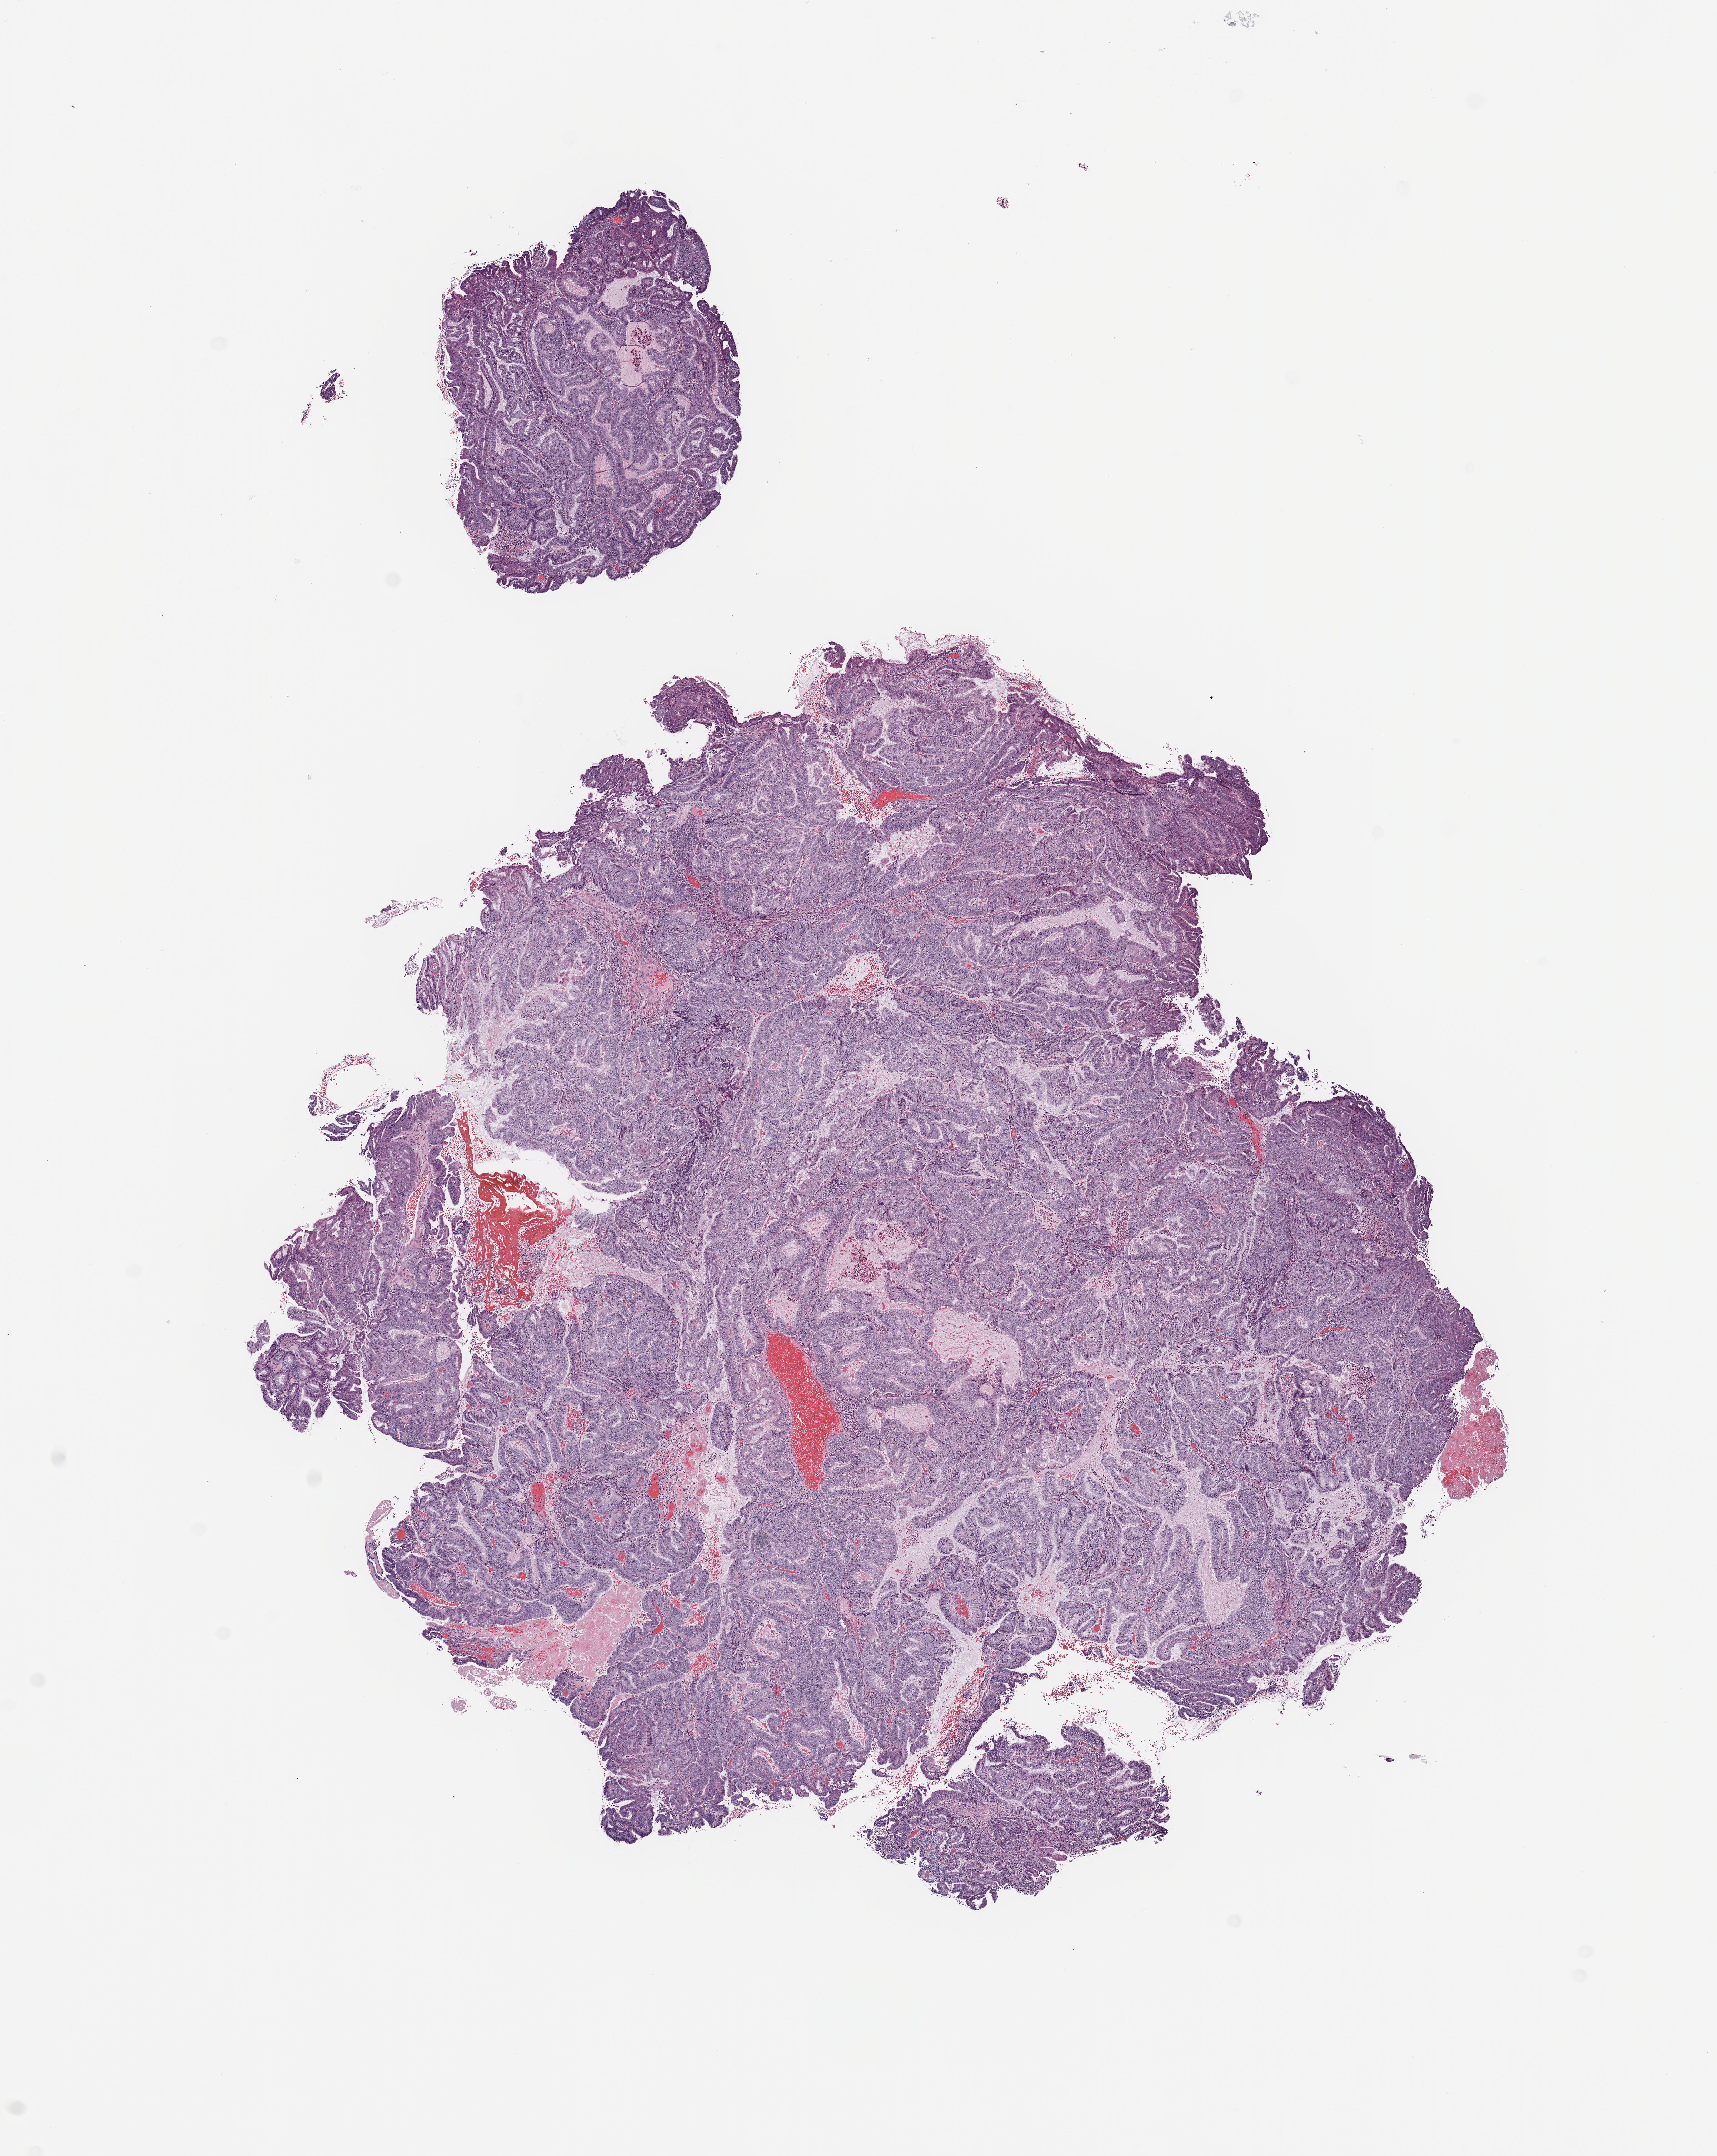
H&E whole-slide image, whole scanned area (about 9.8 x 12.4 mm, from a 20x scan) shown as a low-resolution overview, tumour tissue sample, sampled site: uterus. Female, 84 y/o. Histologic grade: G2 (moderately differentiated). Slide review estimates, as recorded: tumour nuclei 90%, necrosis 2%.
- AJCC pathologic stage: II
- histologic diagnosis: Endometrioid adenocarcinoma, NOS